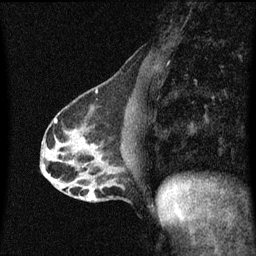
Breast MRI (dynamic contrast-enhanced), one sagittal slice; position 23 of 60 along the scan axis; dynamic contrast-enhanced series, image 2 of 3 at this slice position (ordered by acquisition); 1.5 T; TE 4.2 ms, TR 8.4 ms; 256 × 256 image matrix, field of view 200 × 200 mm. Patient: female, 40 years.
Annotated regions visible in this slice (semi-automatic segmentation, software-assisted and operator-edited):
- analysis volume of interest (the breast-tissue region the enhancement analysis was run in; not a lesion): bounding box [x1, y1, x2, y2] px = [78, 166, 120, 203]
- tumour enhancement mask (voxels above the 70 % enhancement threshold inside the analysis volume of interest): [82, 190, 95, 199]